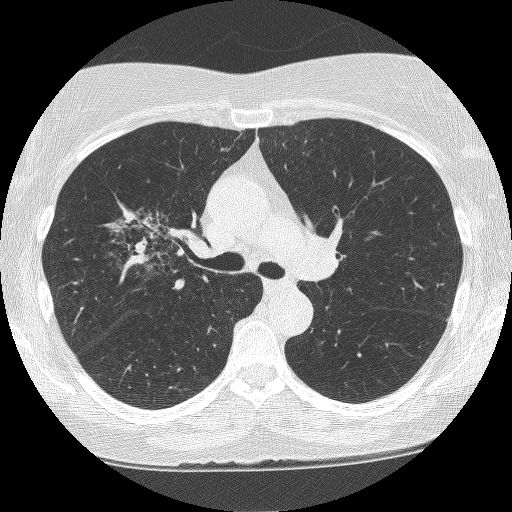
Low-dose screening chest CT, axial slice; second screening round (one year after baseline); lung window (W 1500 / L -600 HU); 1.25 mm slice thickness; 120 kVp. Female, age 64 years at enrolment. Former smoker at enrolment.
Expert reader's lesion annotation, bounding box <115,205,207,292> (left, top, right, bottom; pixels). The screening reader recorded 4 non-calcified nodules or masses ≥4 mm on this exam (right upper lobe, right upper lobe, right upper lobe, left upper lobe); which of them this box marks is not recorded. Lung cancer was diagnosed 381 days after this screen (after the third annual screen): adenocarcinoma, NOS, right upper lobe, right middle lobe, right hilum, stage IV (AJCC 6th edition), 85 mm at pathology.